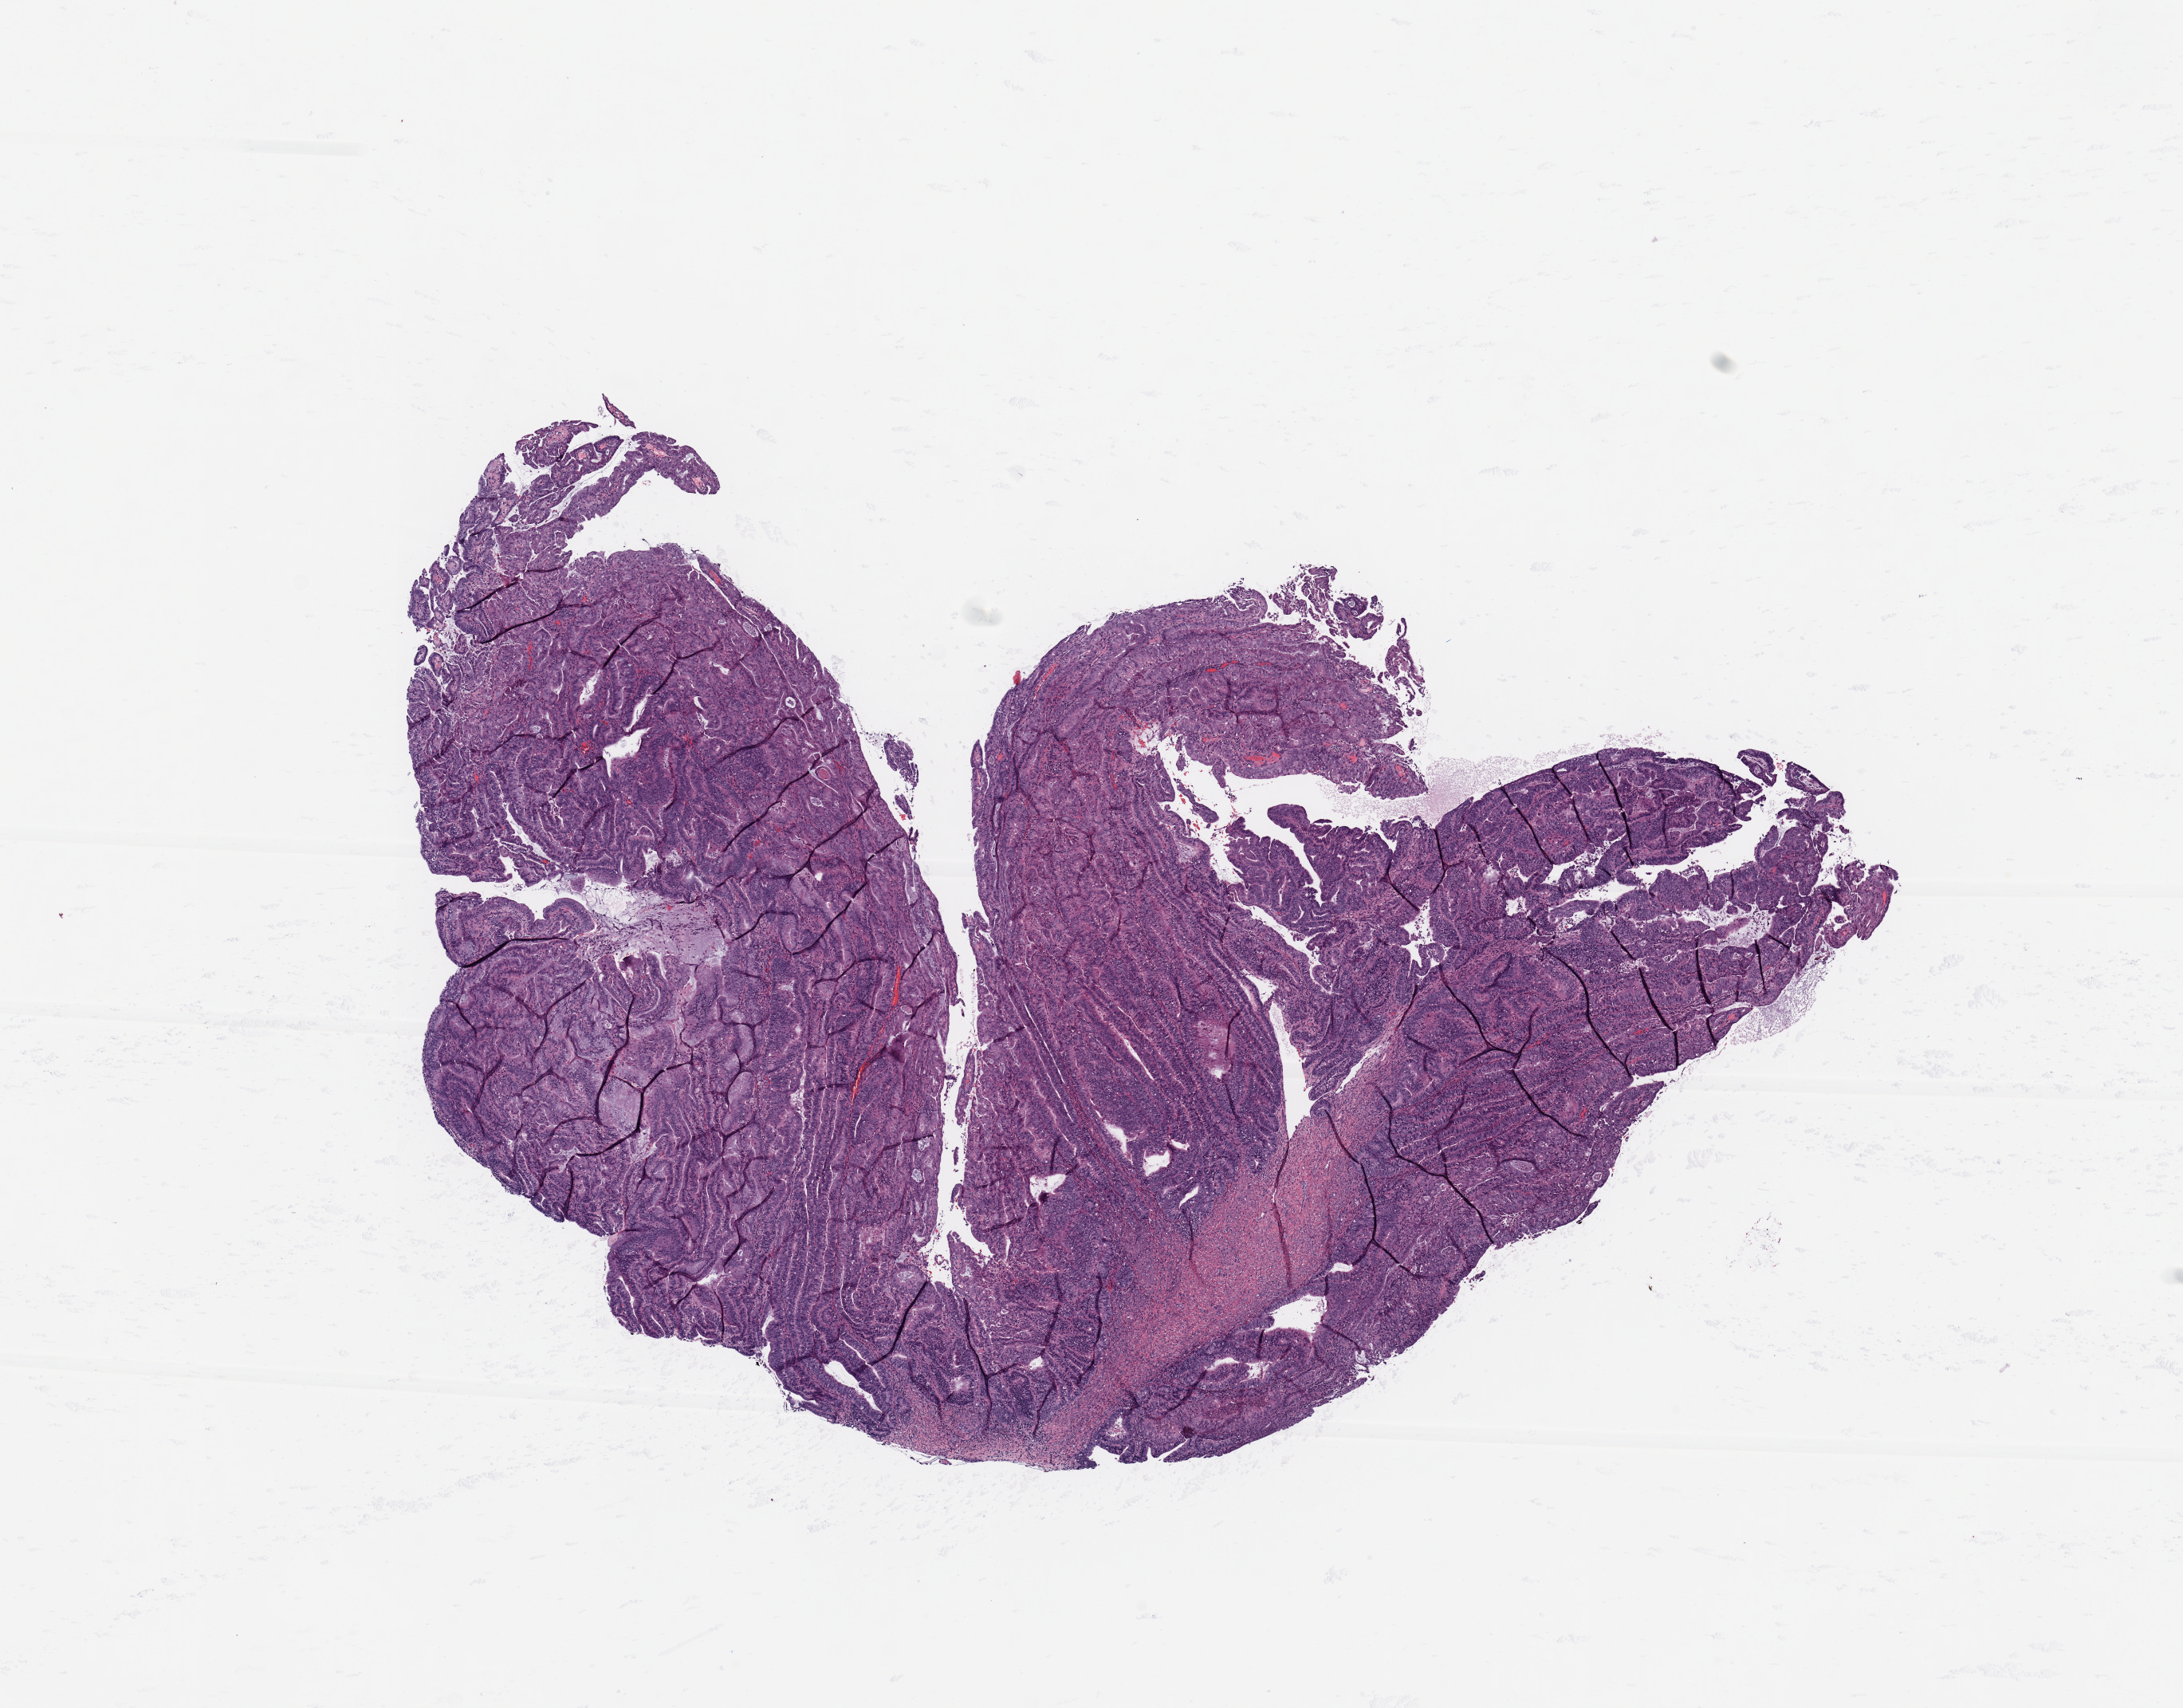
Hematoxylin and eosin (H&E) stained whole-slide image — low-resolution overview of the scanned area, about 10.8 x 8.5 mm (from a 20x scan); tumour tissue sample, uterus. Patient: female, age 64 years. Histologic grade: G2 (moderately differentiated).
* AJCC pathologic stage: III
* diagnosis: Endometrioid adenocarcinoma, NOS
* primary tumour site (as recorded): anterior endometrium